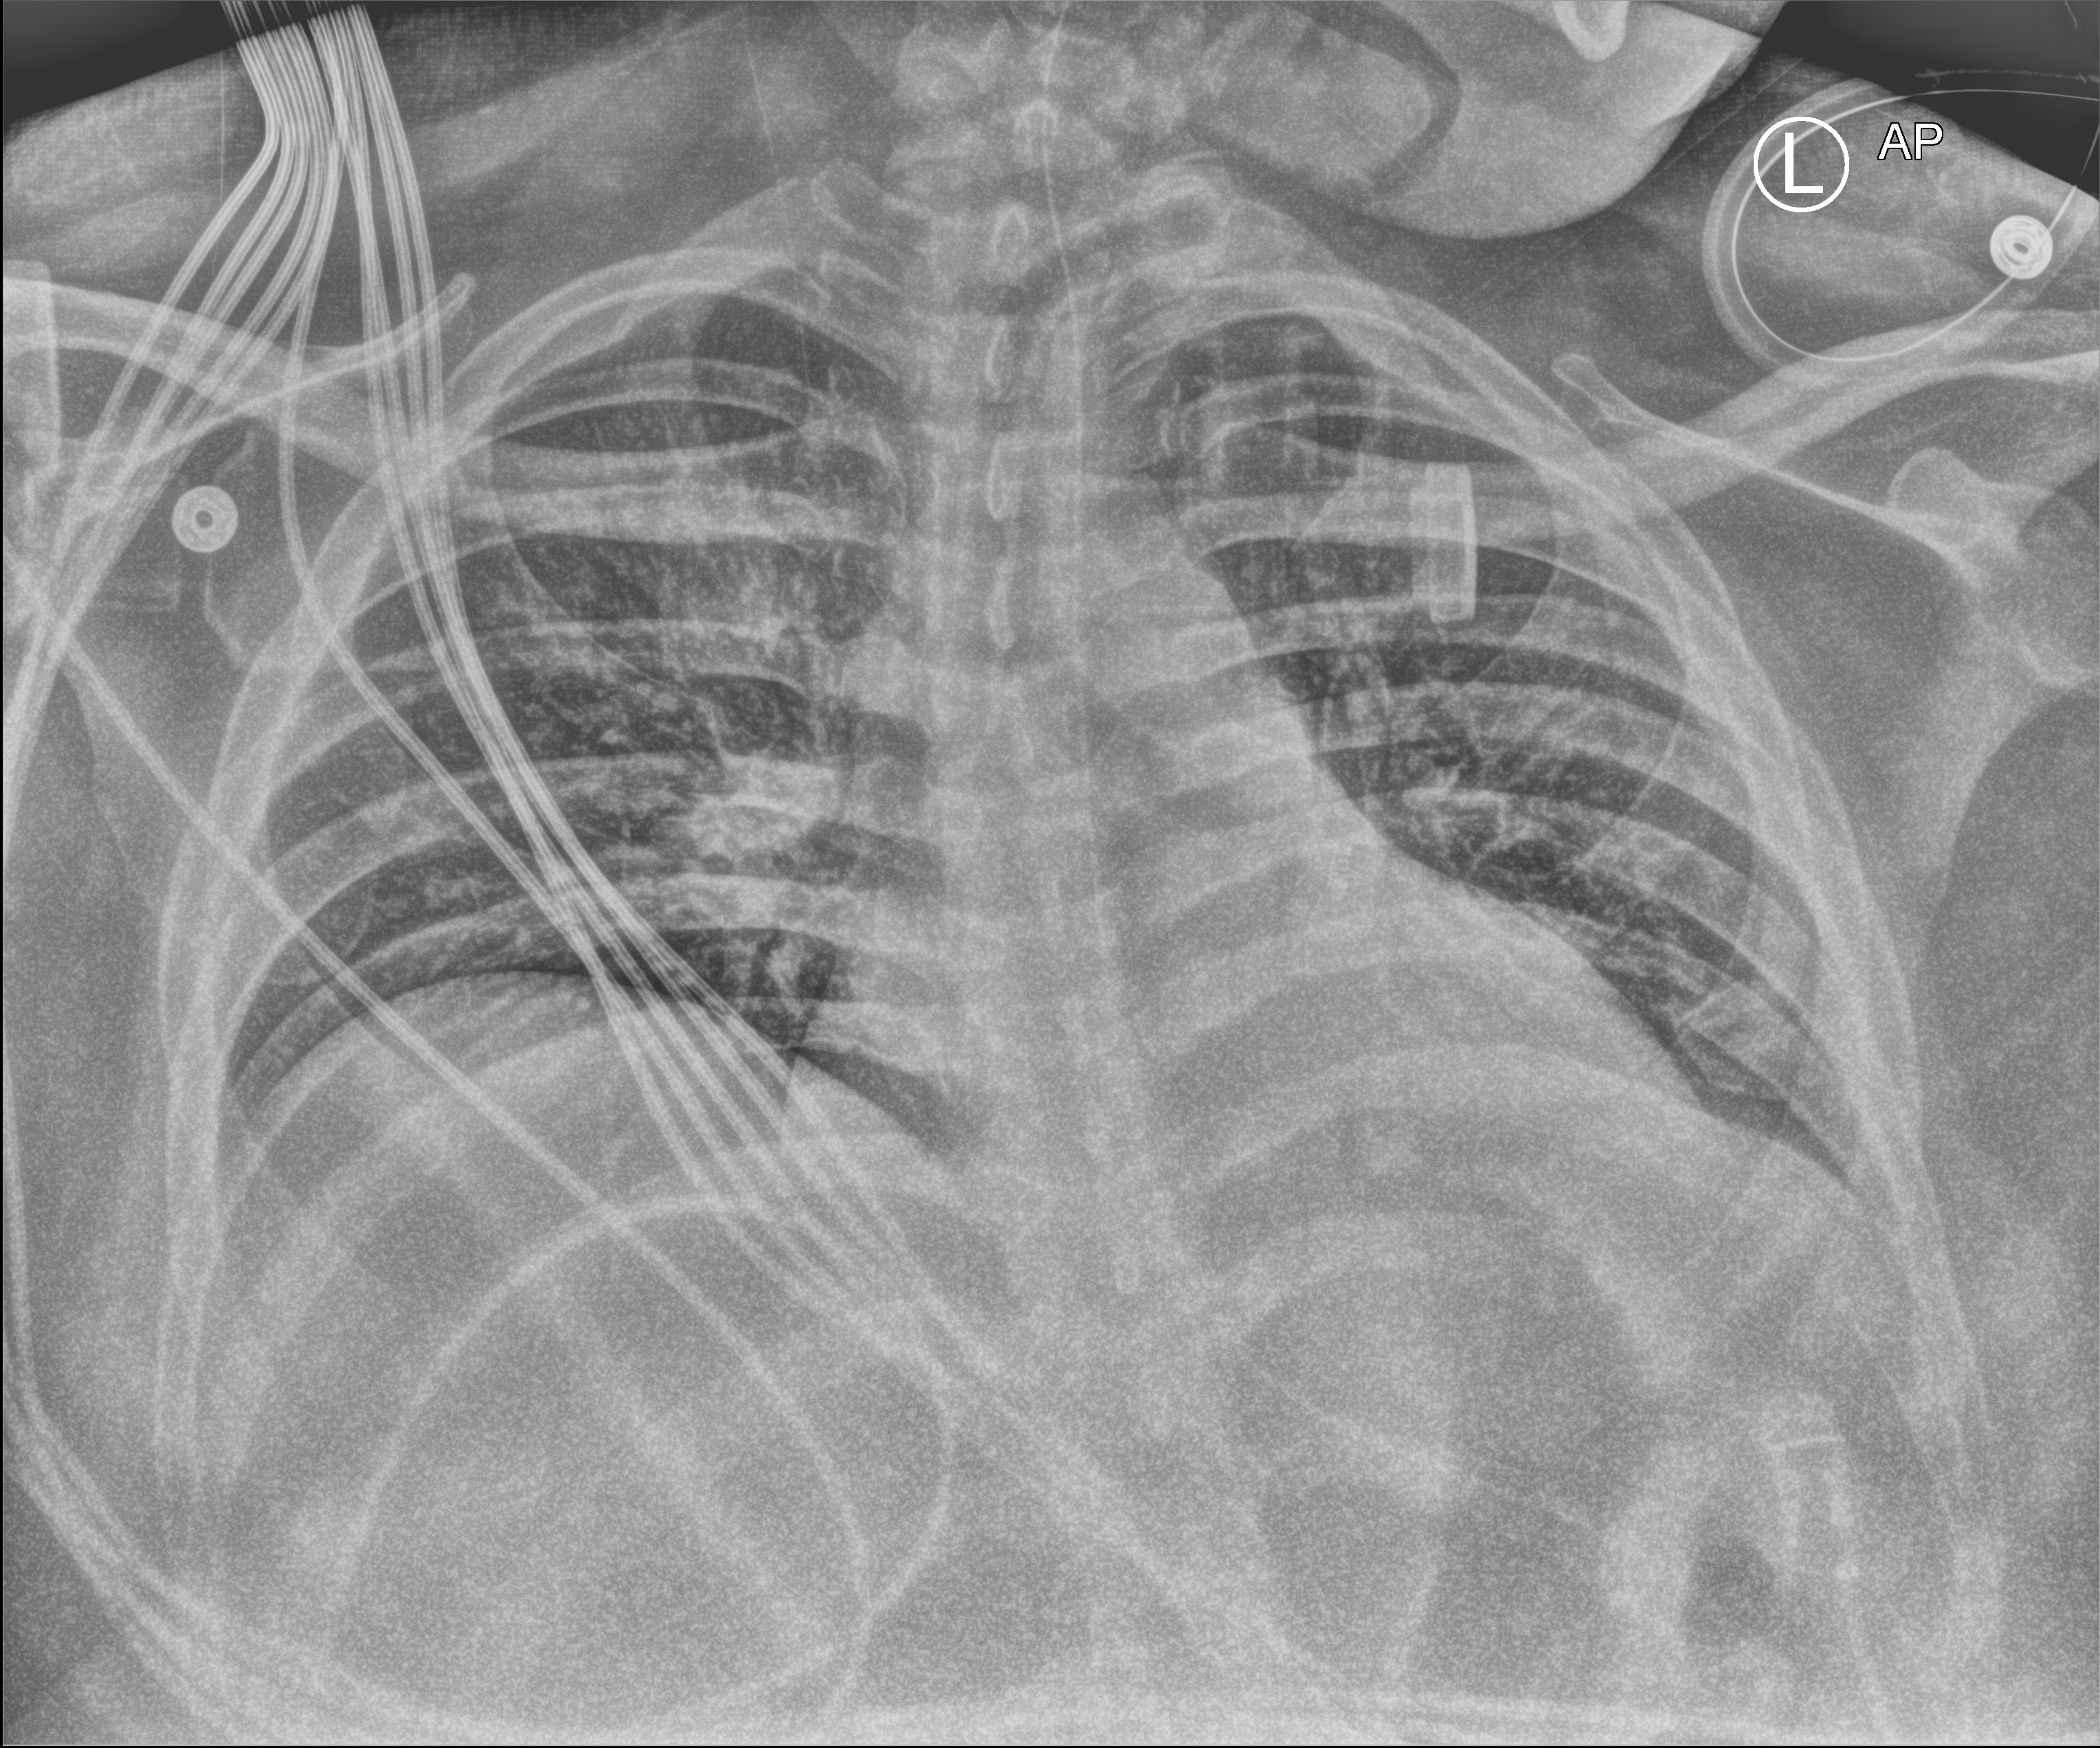
Bedside chest radiograph (computed radiography); anteroposterior (AP) projection. Patient hospitalised with COVID-19; male, aged 18–59 years.
Admission-level facts for this patient (not findings on this image; timing relative to this image not recorded): mechanically ventilated during this hospital stay: yes; admitted to intensive care during this hospital stay: yes.